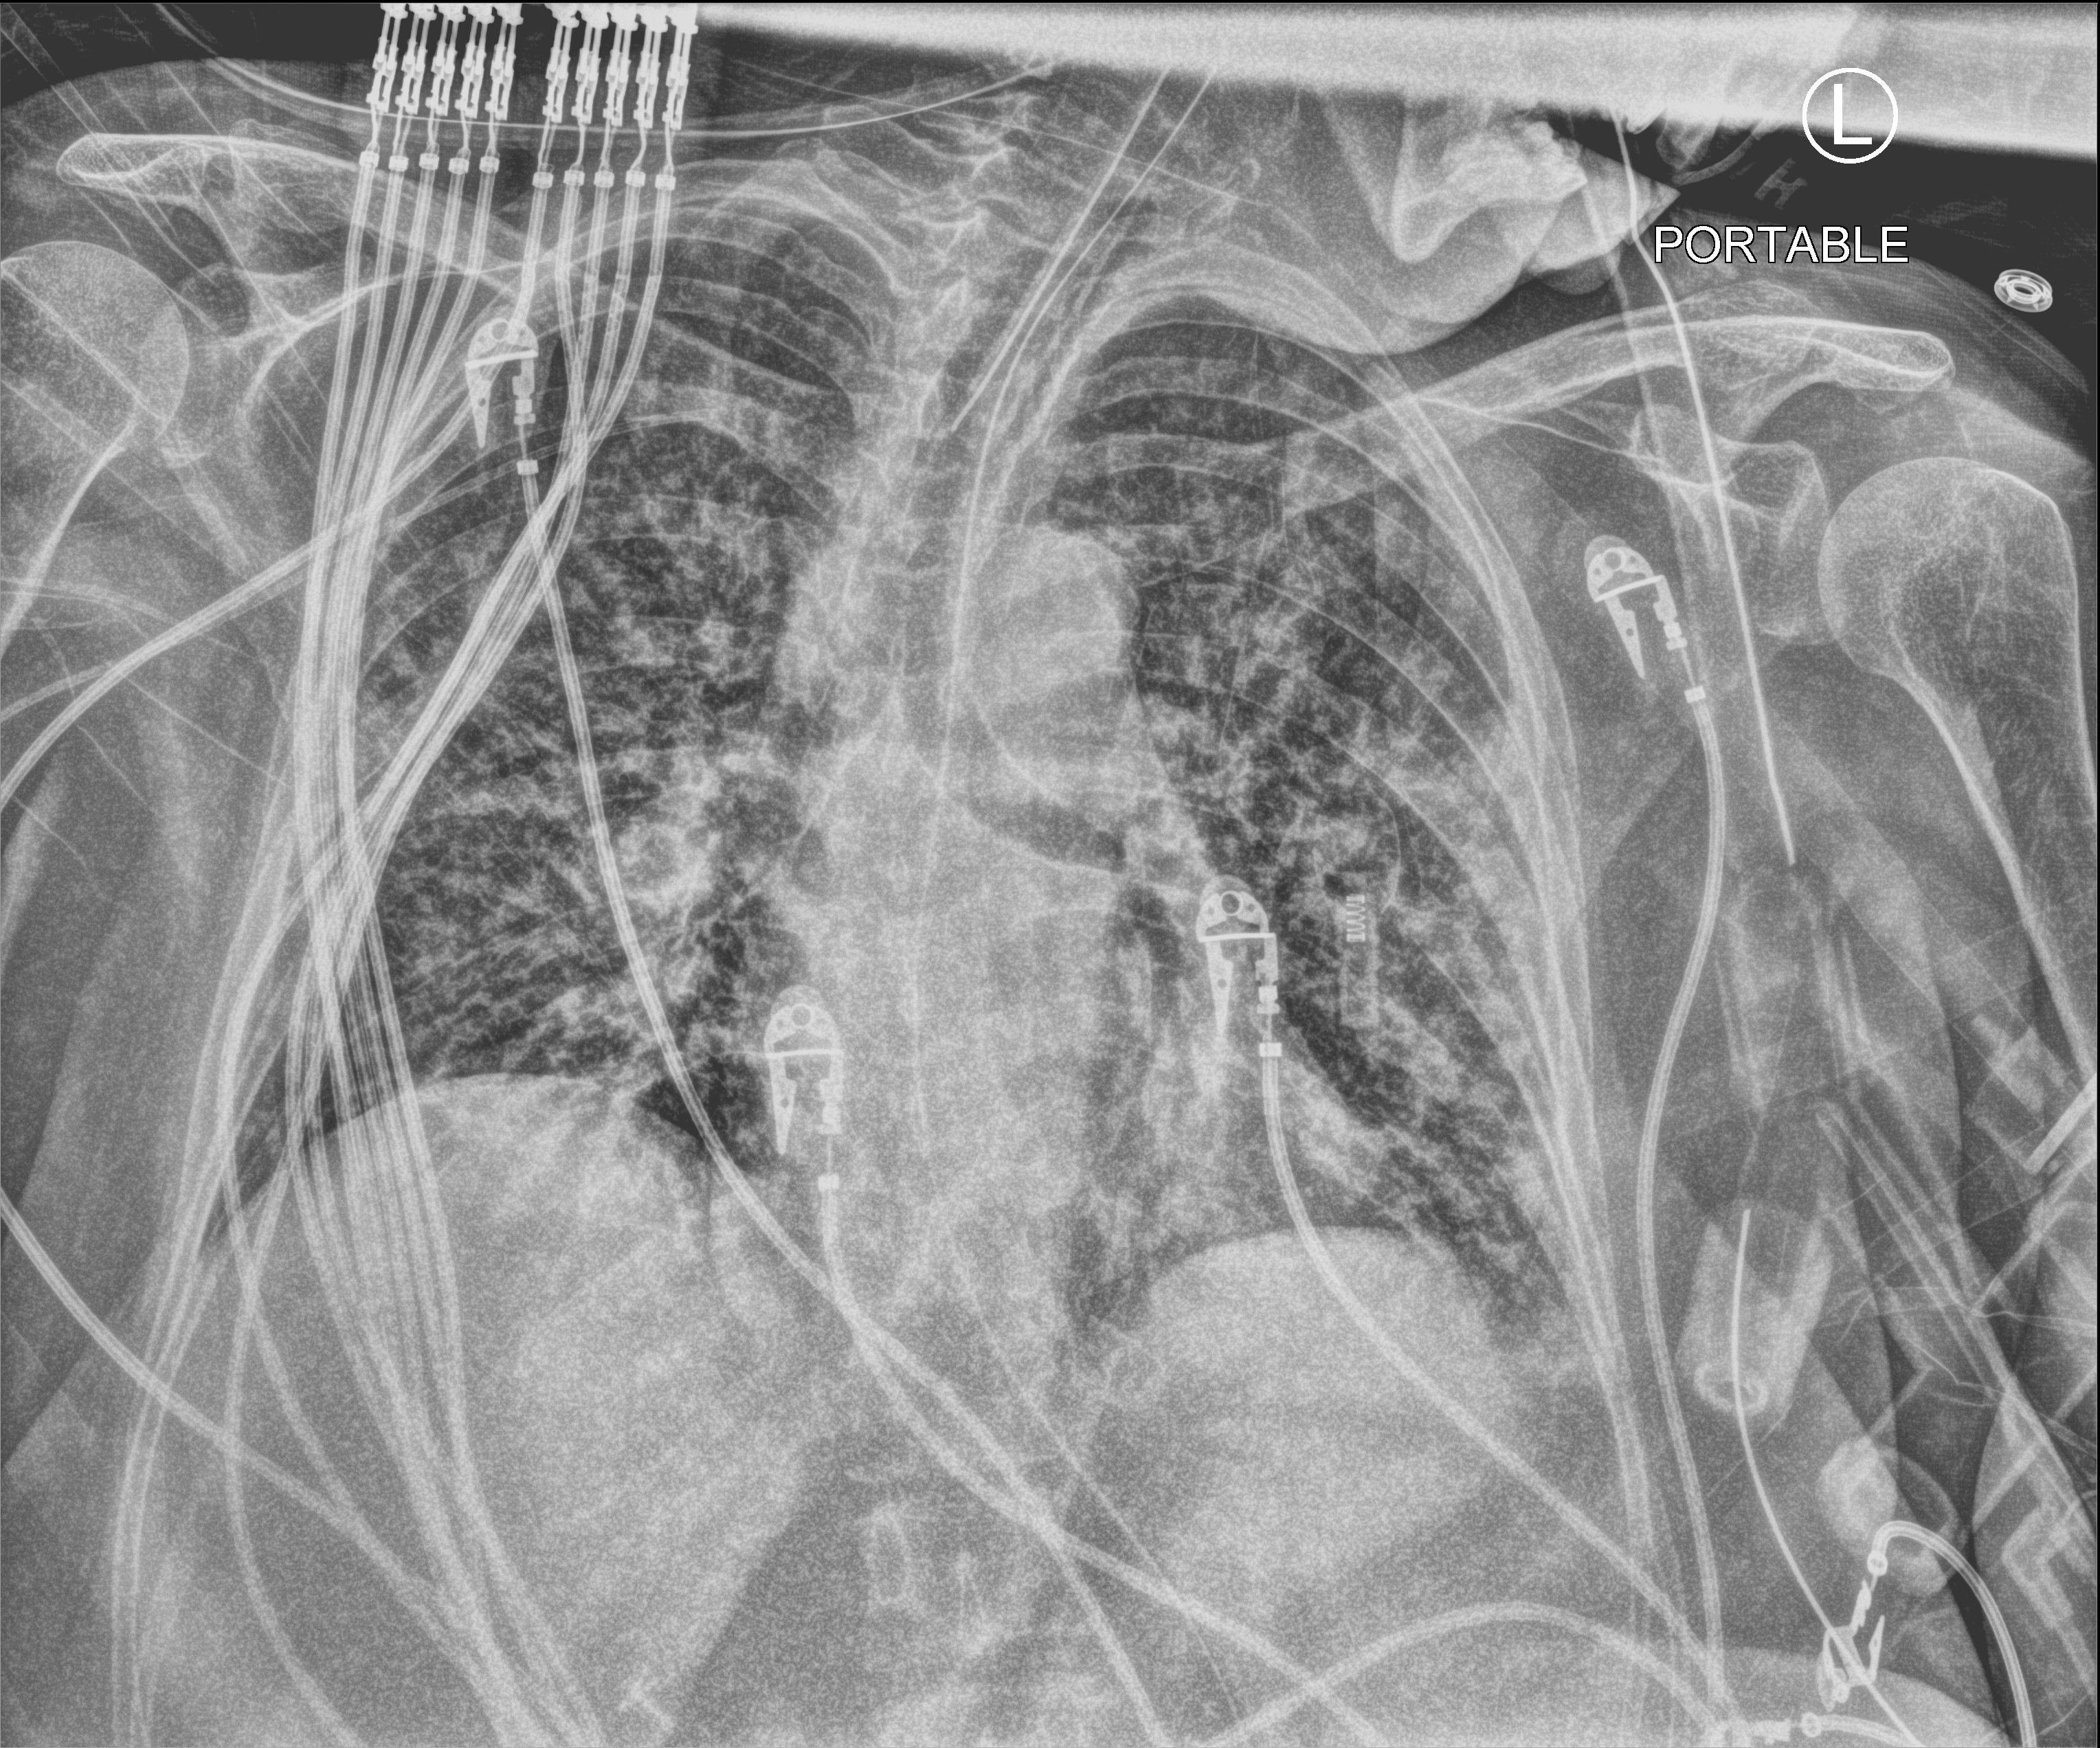
Bedside chest radiograph (computed radiography); anteroposterior (AP) projection. Patient hospitalised with COVID-19; female, aged 18–59 years.
Admission-level facts for this patient (not findings on this image; timing relative to this image not recorded): other chronic lung disease (admission record): no; mechanically ventilated during this hospital stay: yes.